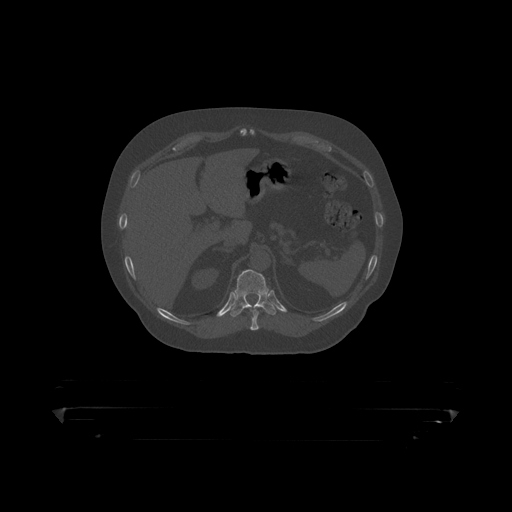
CT including the spine, one axial slice; slice 200 of 390 in the series (ordered by position); reconstruction kernel STANDARD; 120 kVp; bone window (W 1800 / L 400 HU); 1.25 mm slice thickness; 512 × 512 image matrix. Male patient, age 60 years. From the clinical record (not read from this slice): primary cancer: prostate.
Annotated regions visible in this slice (semi-automatic segmentation, software-assisted and operator-edited):
- T10 vertebra: box from (x=250, y=307) to (x=259, y=319) px
- T11 vertebra: (x=230, y=270)–(x=283, y=316)